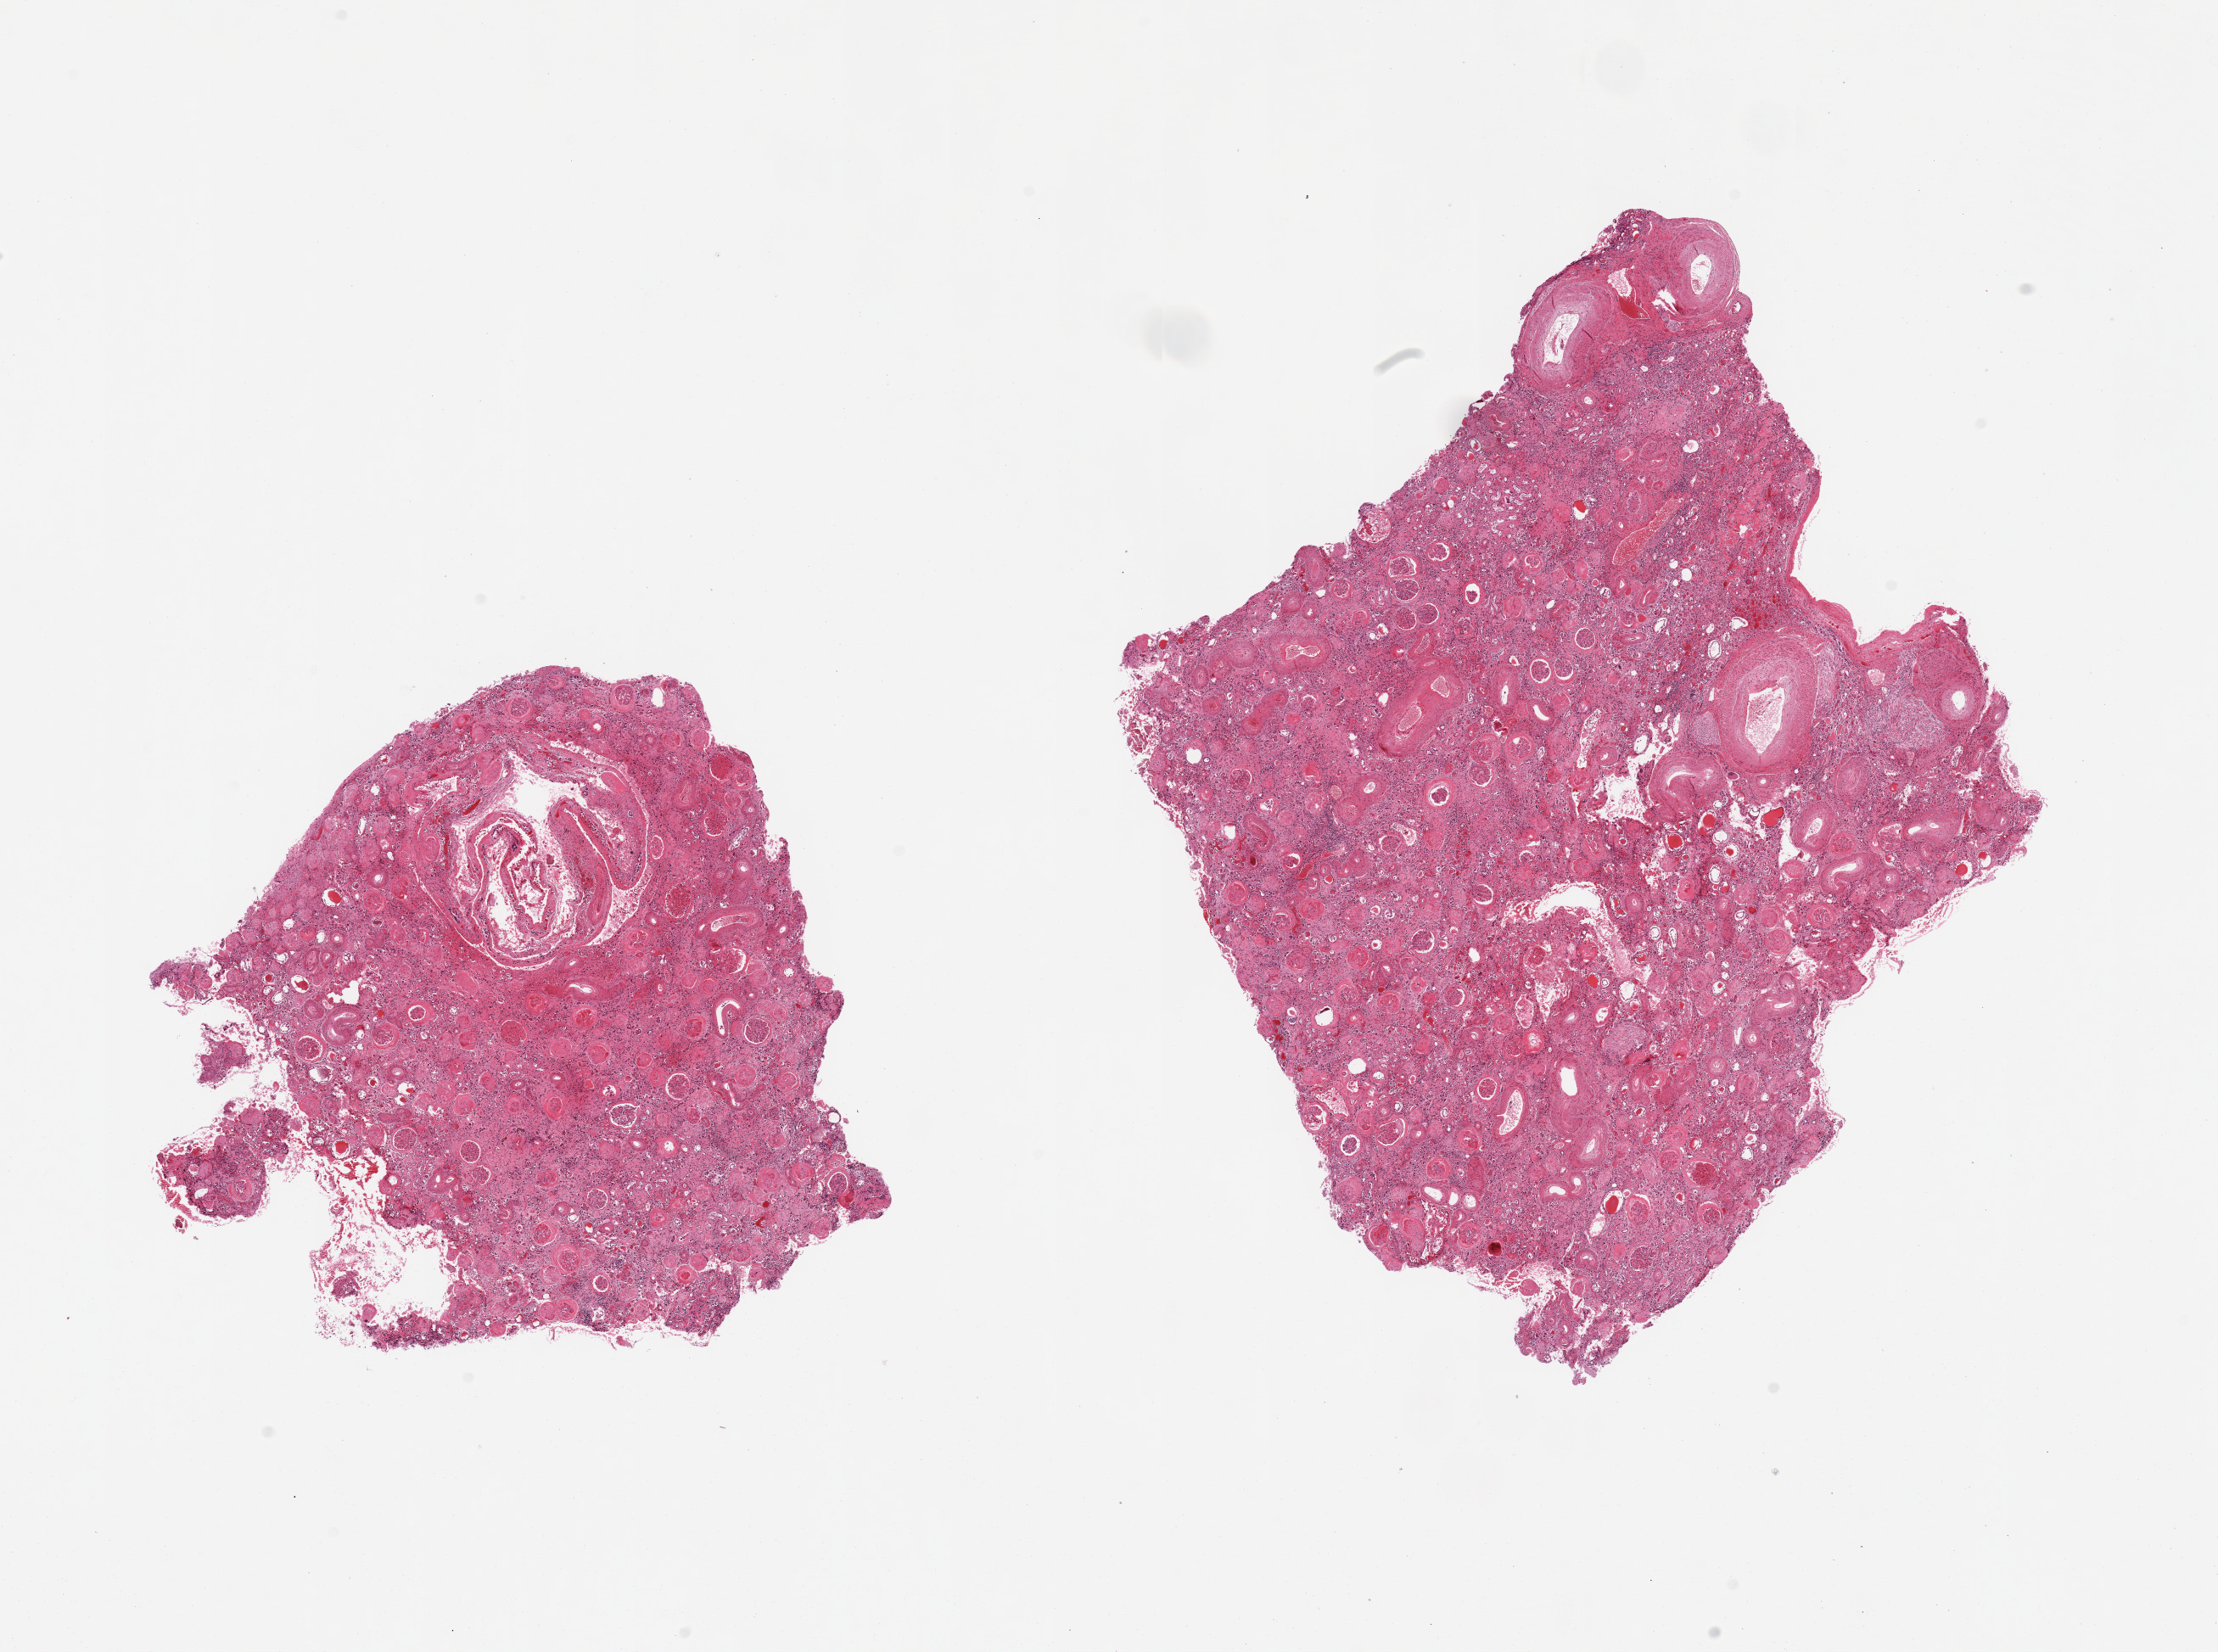
Hematoxylin and eosin (H&E) whole-slide image — low-resolution overview of the scanned area, about 20.7 x 15.4 mm. PAXgene-fixed, paraffin-embedded tissue. Sampled site (target tissue): renal cortex. Tissue donor sample. Female donor.
Review note (as recorded): 2 pieces; extensive vascular, parenchymal and glomerular sclerosis [c/w renal failure].